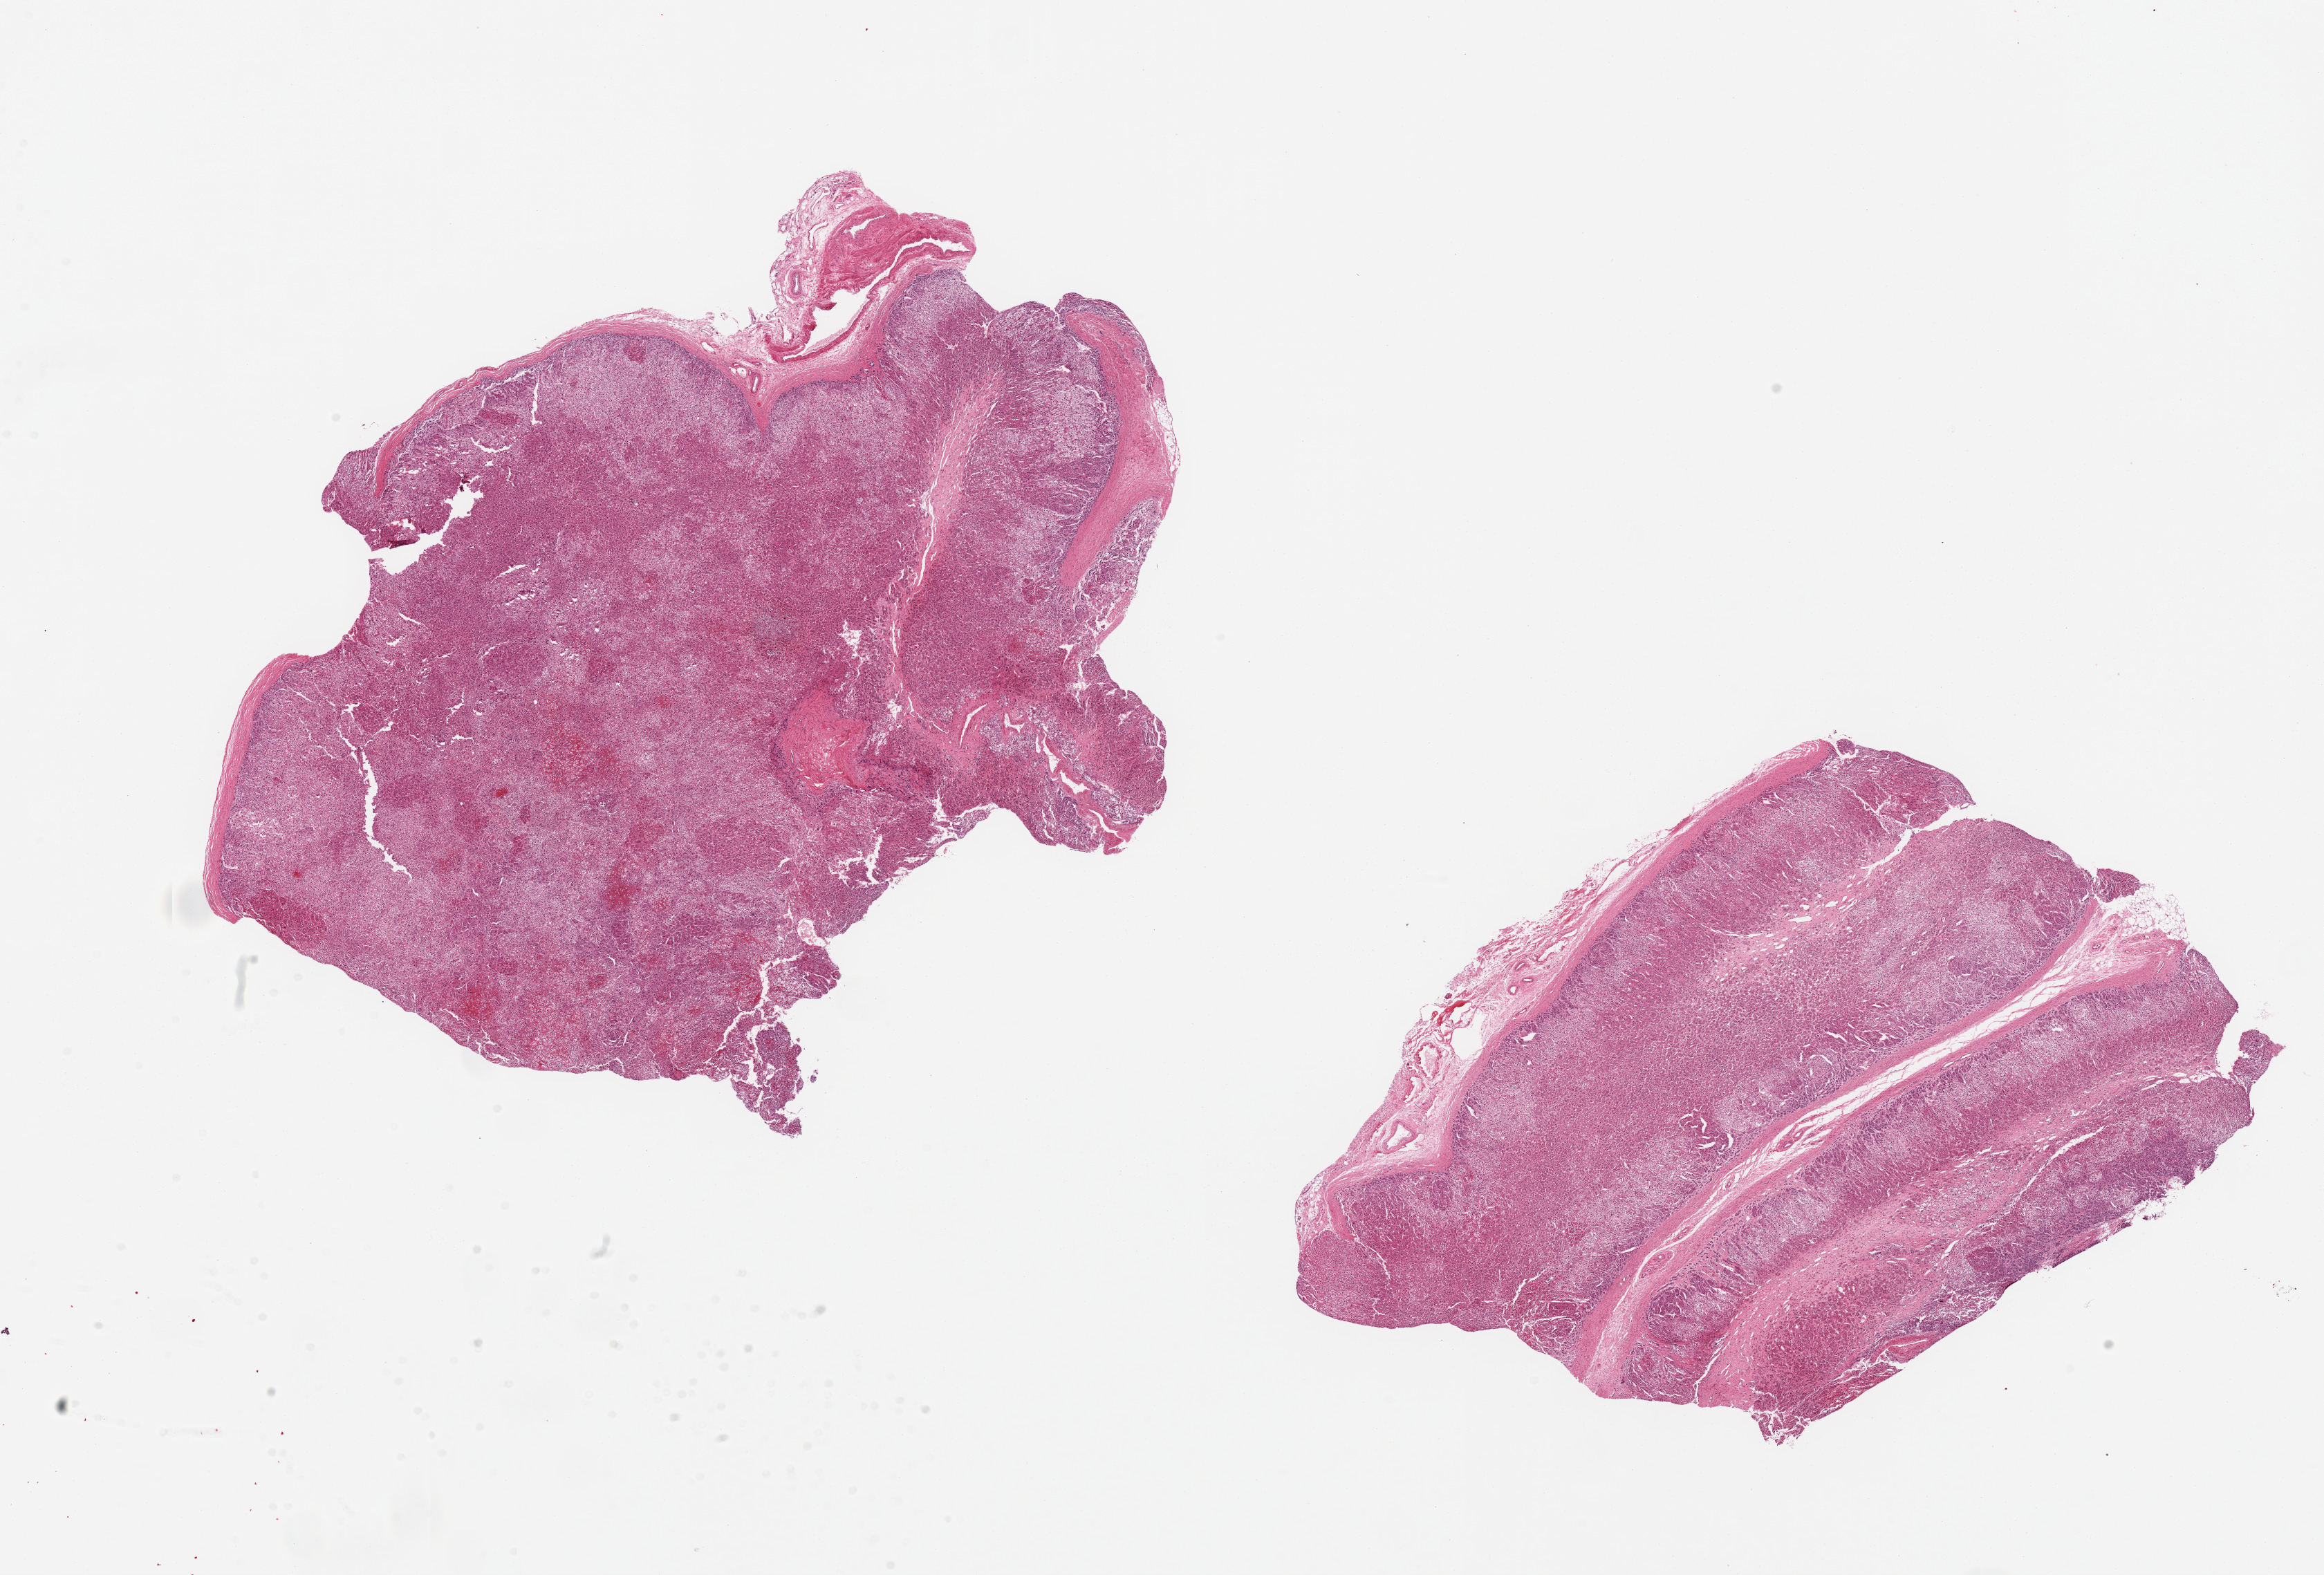
Digitized haematoxylin and eosin-stained section — a low-resolution overview of the entire scanned area, about 26.6 x 18.0 mm. PAXgene-fixed paraffin-embedded (PFPE) section. Target tissue: adrenal gland. Donor tissue sample. Male donor.
* pathologist's review note for this sample: 2 pieces; mildly to moderately autolyzed adrenal cortex